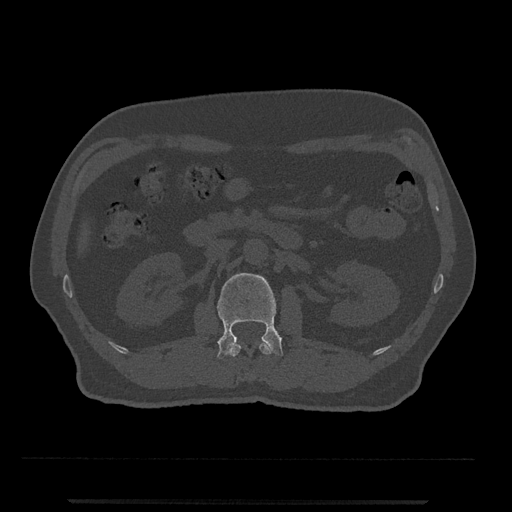
CT including the spine, one axial slice; slice 286 of 797 in the series (ordered by position); 120 kVp; bone window (W 1800 / L 400 HU); 0.5 mm slice thickness; 512 × 512 image matrix. Male patient, age 63 years. From the clinical record (not read from this slice): primary cancer: prostate.
Outlined on this slice (semi-automatically segmented with operator editing):
- L1 vertebra: box from (x=231, y=340) to (x=273, y=356) px
- L2 vertebra: (x=217, y=273)–(x=283, y=358)